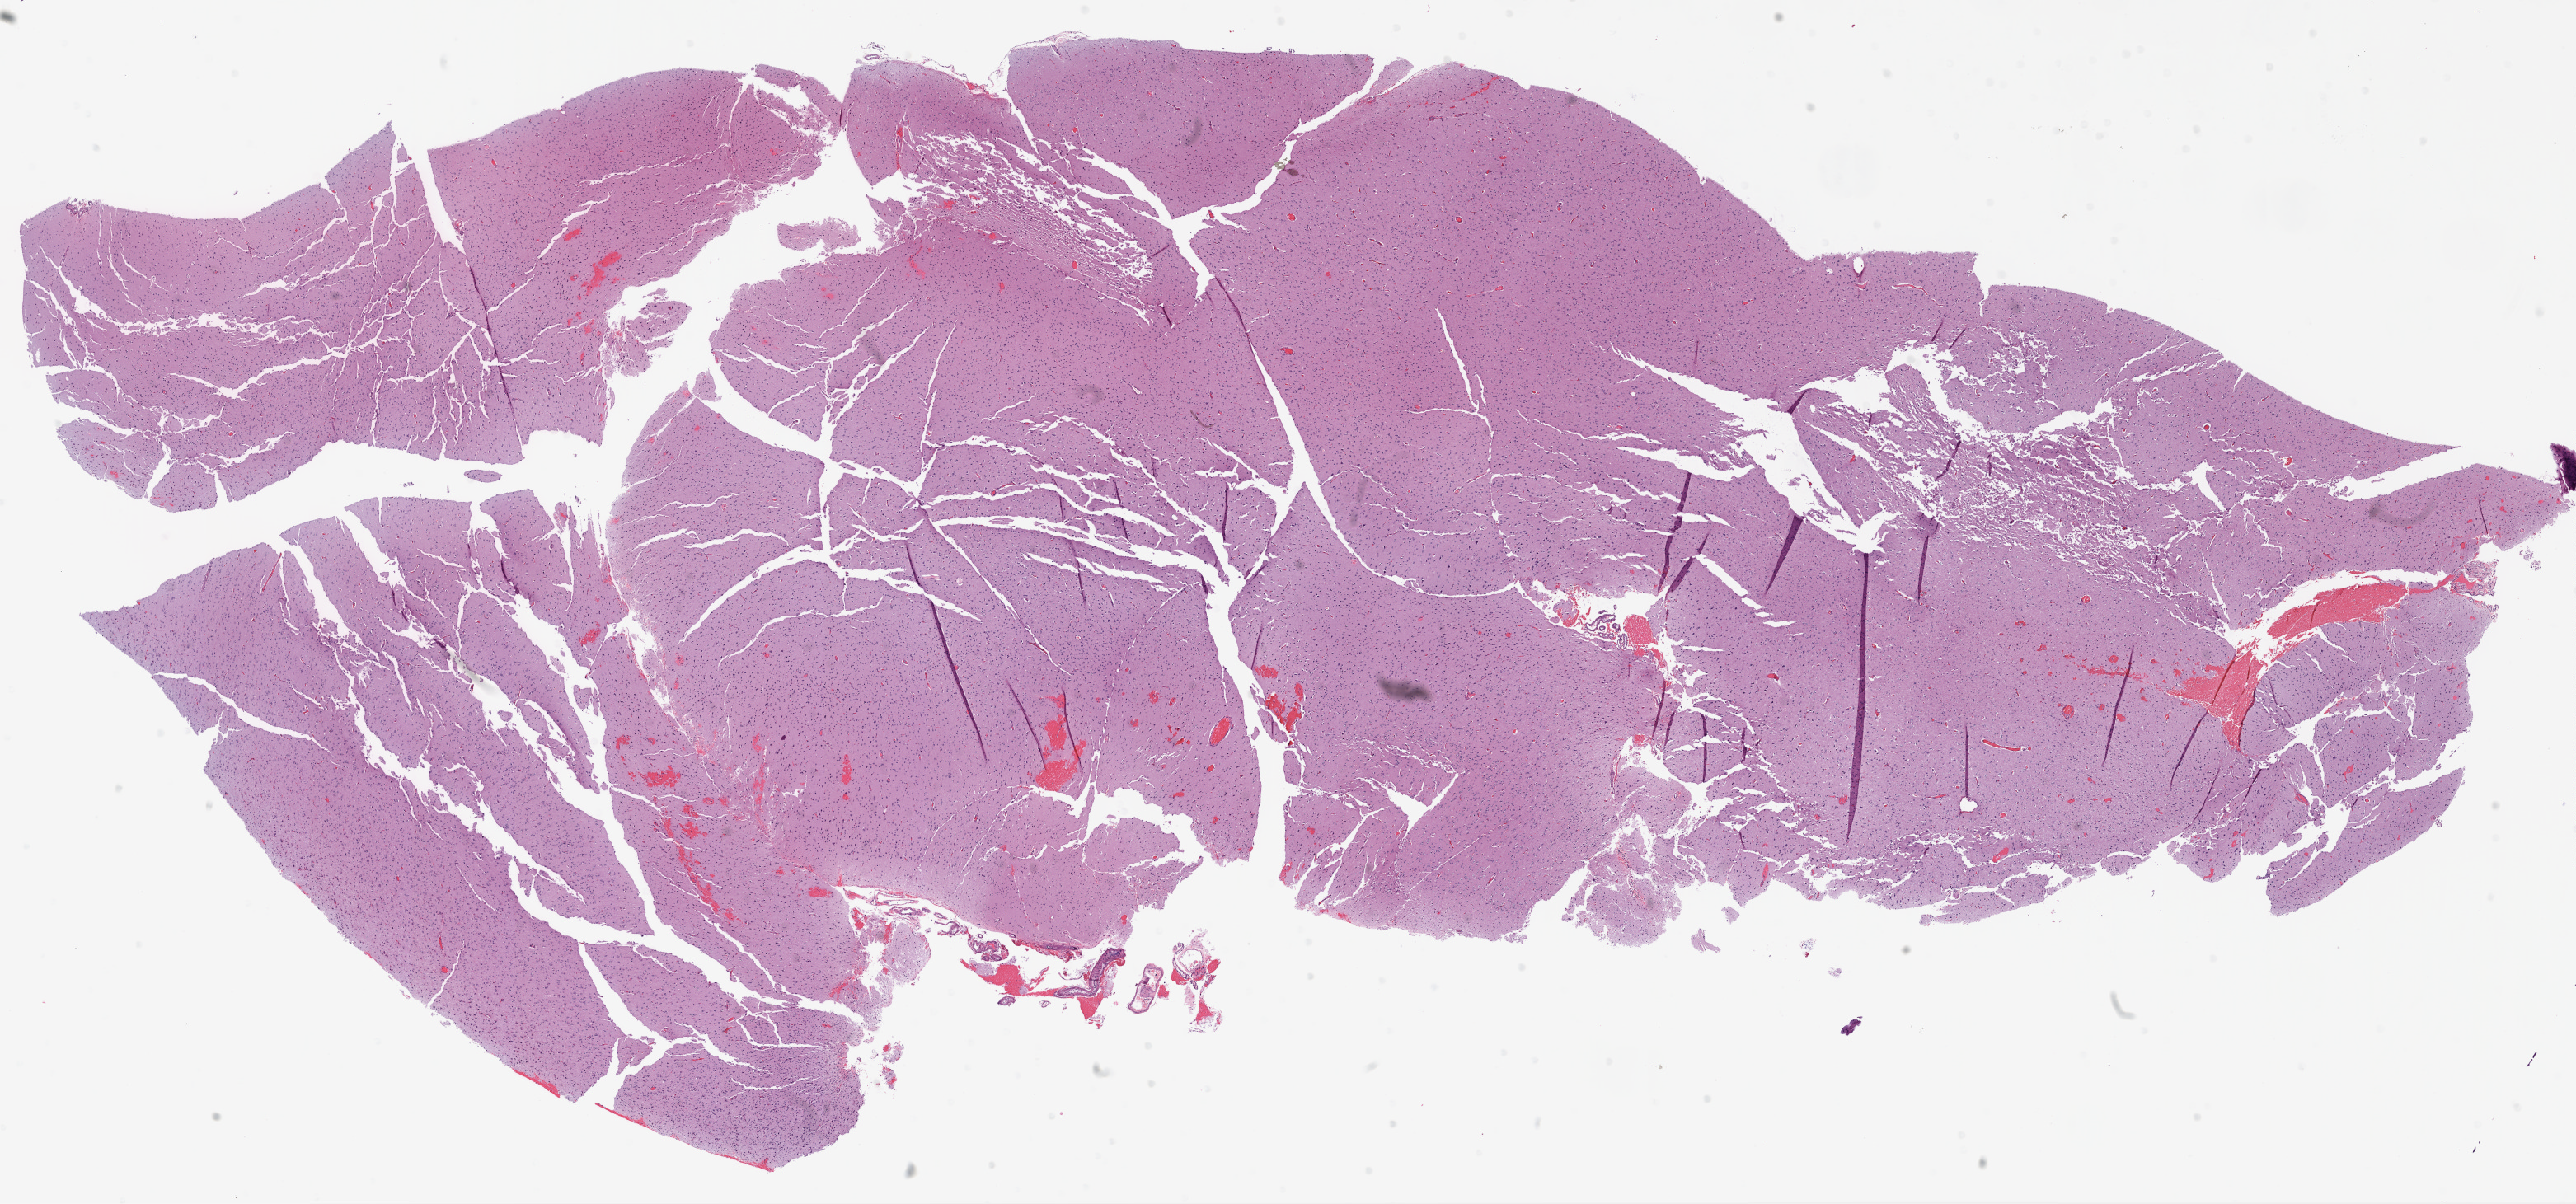
Digitized H&E tissue section (whole slide), whole scanned area (about 25.1 x 11.7 mm, slide scanned at 20x) shown as a low-resolution overview. Formalin-fixed paraffin-embedded (FFPE) diagnostic section. Primary tumour sample from the brain. Male patient; age at initial diagnosis 57 years.
Pathologic diagnosis: Glioblastoma.